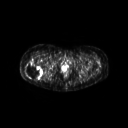
FDG PET of an extremity soft-tissue mass (from a PET/CT study), one axial slice; position 41 of 267 along the scan axis; 3.27 mm slice thickness; 128 × 128 image matrix, field of view 600 × 600 mm. Patient: female, 57 years. Case-level facts recorded for this patient, not image findings: histological type: epithelioid sarcoma with vascular differentiation; site of the primary tumour: right buttock.
Structures marked on this image (expert contour drawn on MRI and transferred to this co-registered scan by the dataset authors):
- gross tumour volume (mass): bounding box <24,60,44,80> (left, top, right, bottom; pixels)